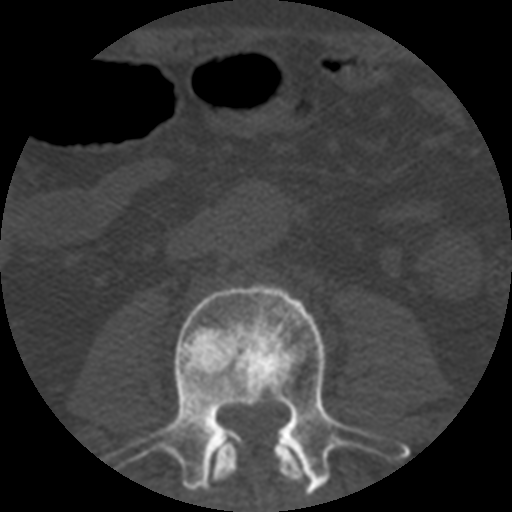
CT including the spine, one axial slice. Position 127 of 508 along the scan axis. 120 kVp. Bone window (W 1800 / L 400 HU). 1.25 mm slice thickness. 512 × 512 image matrix, field of view 160 × 160 mm. Patient age 57 years. Case-level facts recorded for this patient, not image findings: primary cancer: prostate.
Annotated regions visible in this slice (semi-automatic segmentation, software-assisted and operator-edited):
- L2 vertebra: box from (x=210, y=436) to (x=310, y=496) px
- L3 vertebra: (x=102, y=285)–(x=410, y=496)